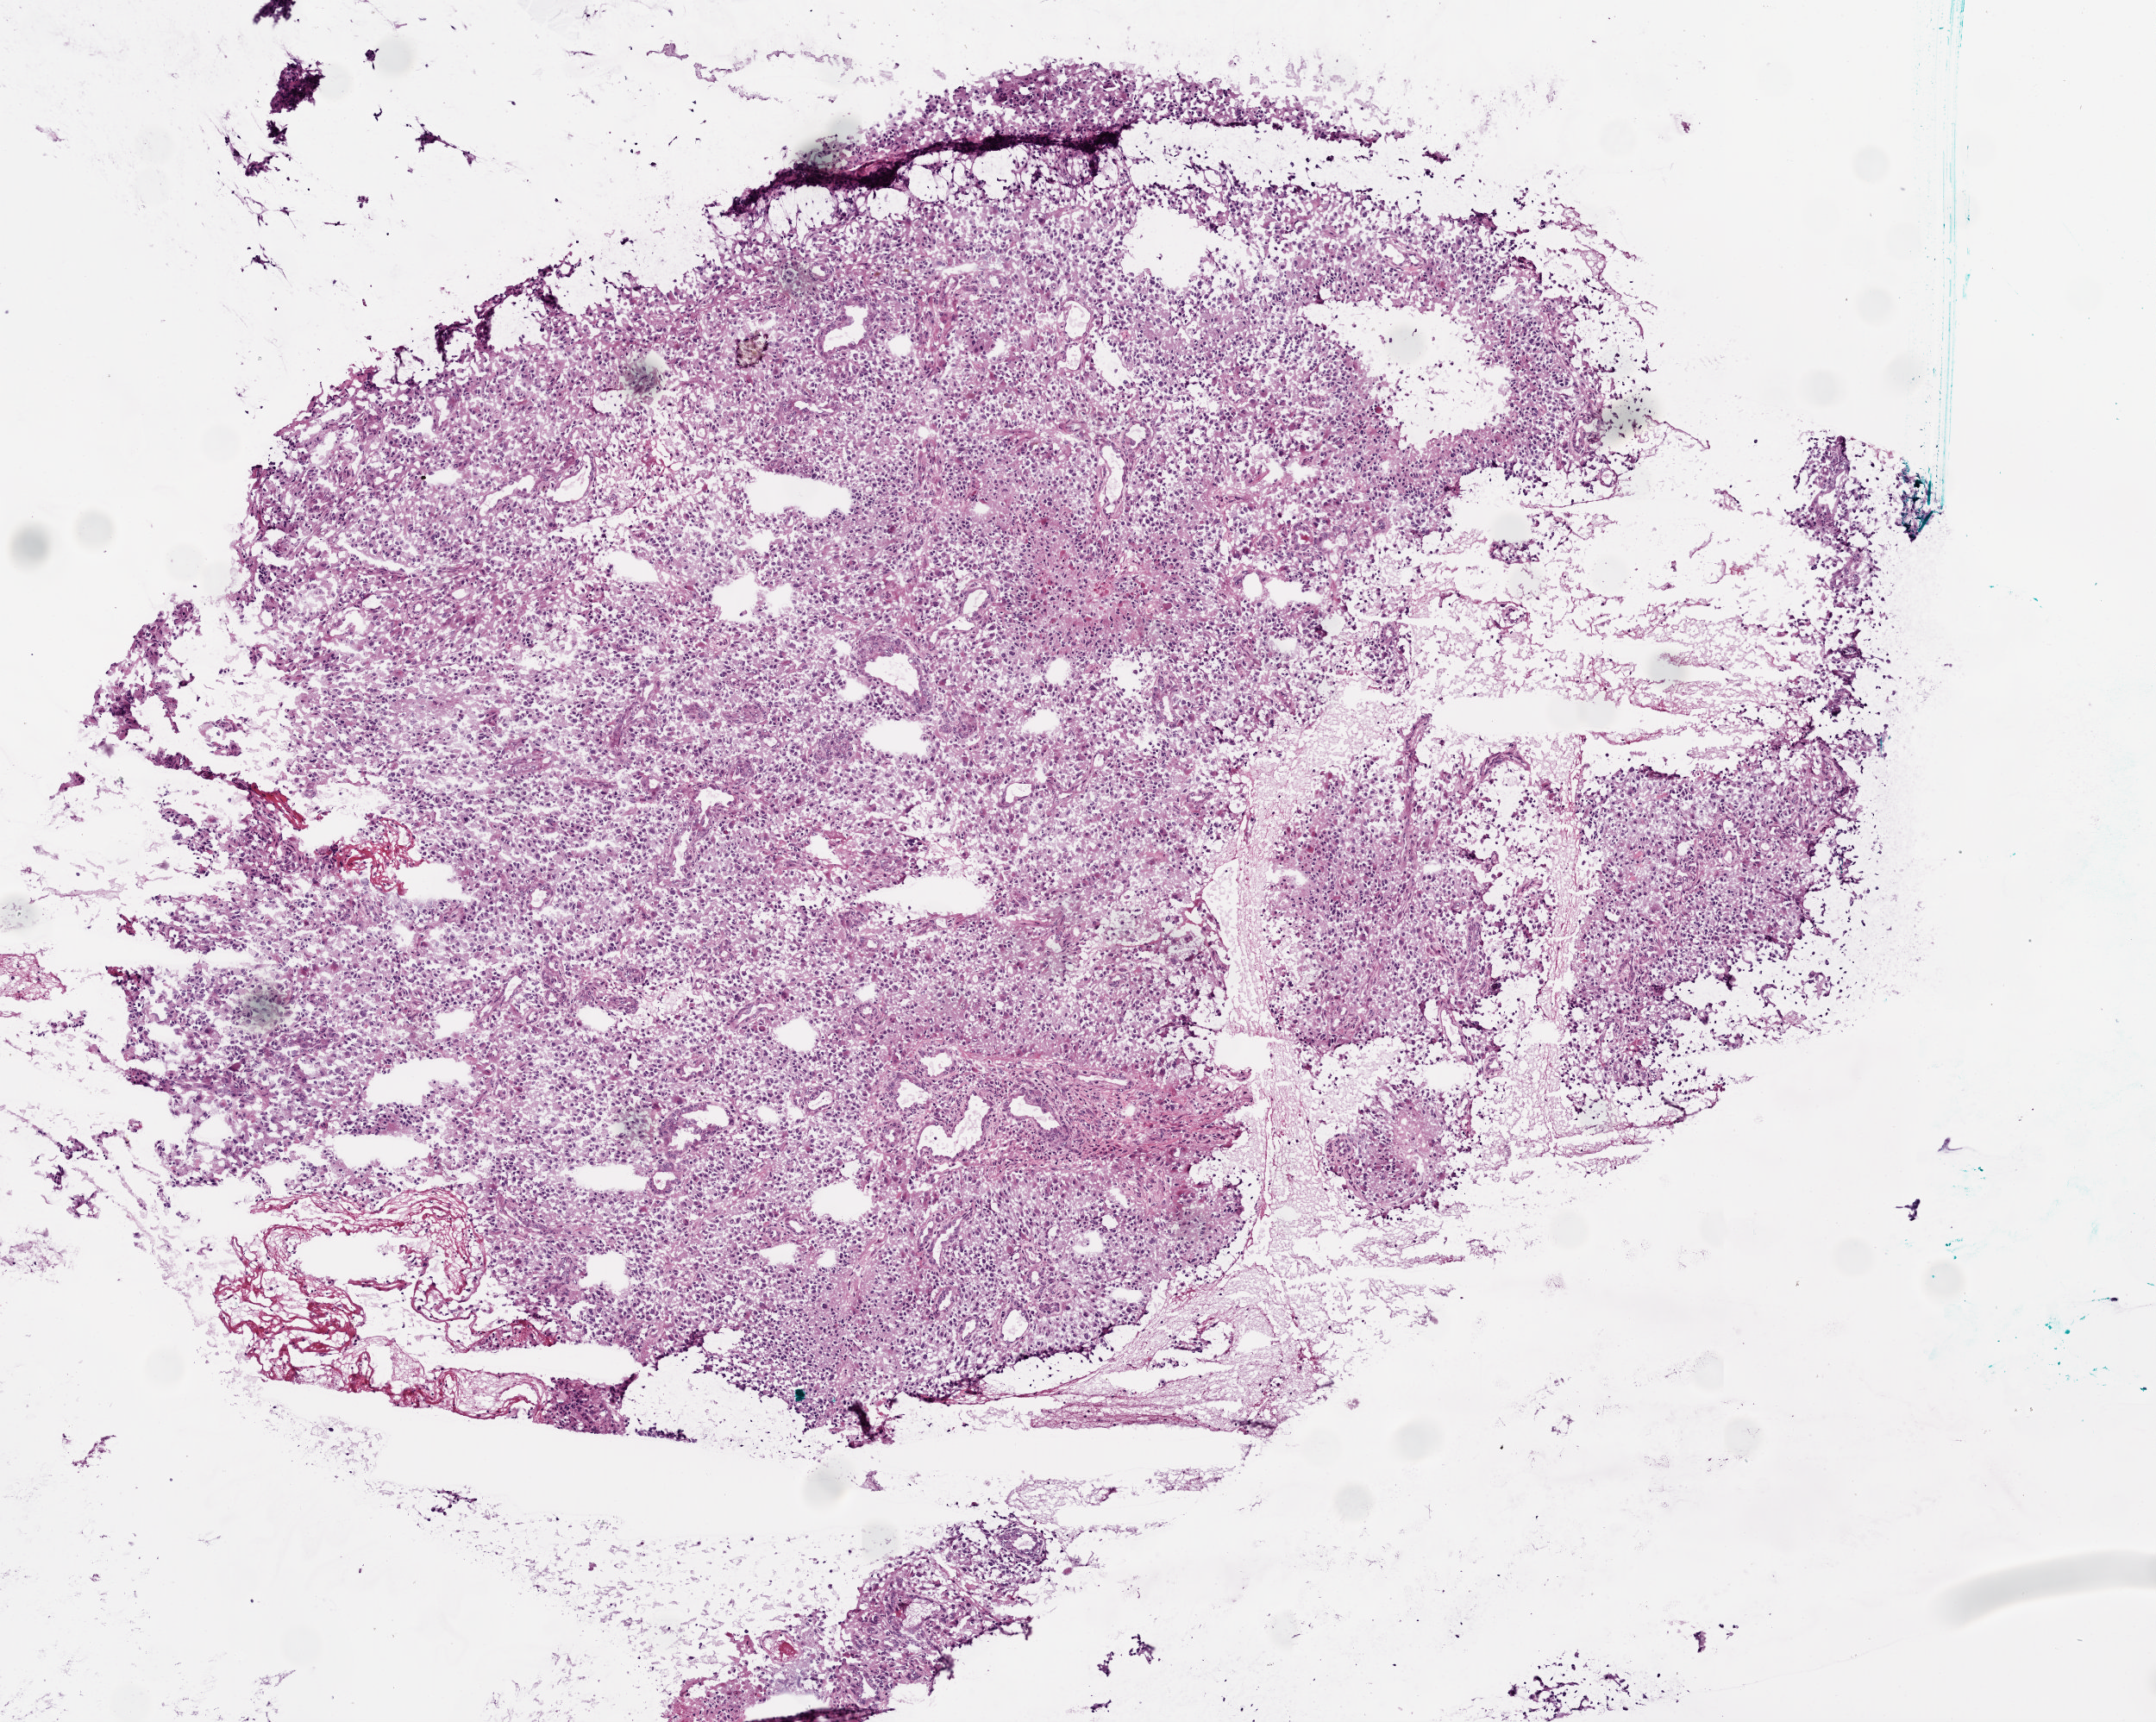
H&E whole-slide image, low-resolution overview of the scanned area, about 5.0 x 4.0 mm (from a 20x scan); frozen section from the bottom of the tissue portion; primary tumour sample from the brain. Male patient; age at initial diagnosis 55 years. Composition of this section per pathologist review: tumour cells 95%, tumour nuclei 95%, normal cells 0%, stromal cells 0%, necrosis 5%.
• diagnosis: Glioblastoma